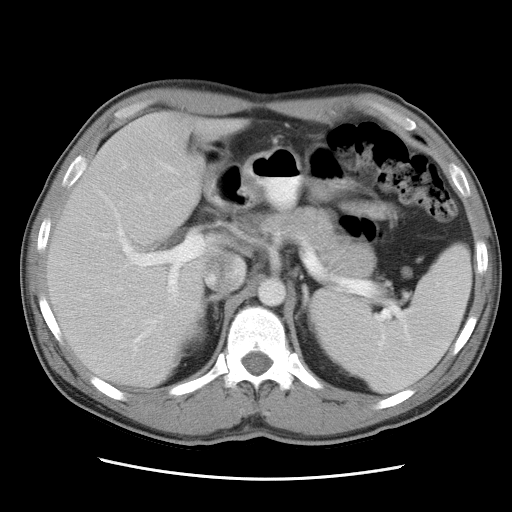
Contrast-enhanced abdominal CT, one axial slice. Slice 19 of 34 in the series (ordered by position). Reconstruction kernel STANDARD. 120 kVp. Intravenous contrast given. Soft-tissue window (W 400 / L 40 HU). 7.5 mm slice thickness. 512 × 512 image matrix. Male patient, age 40 years. Case-level facts recorded for this patient, not image findings: diagnosis: colorectal cancer liver metastases, imaged before liver resection; multiple liver metastases: yes; largest metastasis: 1.5 cm; disease in both lobes: yes.
Annotated regions visible in this slice (manually delineated by an expert):
- liver: box from (x=48, y=112) to (x=242, y=386) px
- planned liver remnant (the part of the liver to remain after resection): (x=48, y=112)–(x=241, y=386)
- portal vein (with intrahepatic branches): (x=85, y=187)–(x=205, y=325)